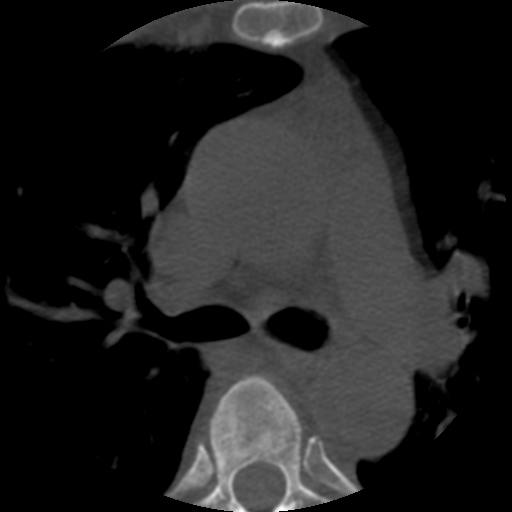
CT including the spine, one axial slice; position 380 of 508 along the scan axis; reconstruction kernel STANDARD; 120 kVp; bone window (W 1800 / L 400 HU); 1.25 mm slice thickness; 512 × 512 image matrix, field of view 160 × 160 mm. Patient age 57 years. Case-level facts recorded for this patient, not image findings: primary cancer: prostate.
Outlined on this slice (semi-automatic segmentation, software-assisted and operator-edited):
- T5 vertebra: bounding box (x1, y1, x2, y2) in pixels: (200, 374, 330, 512)